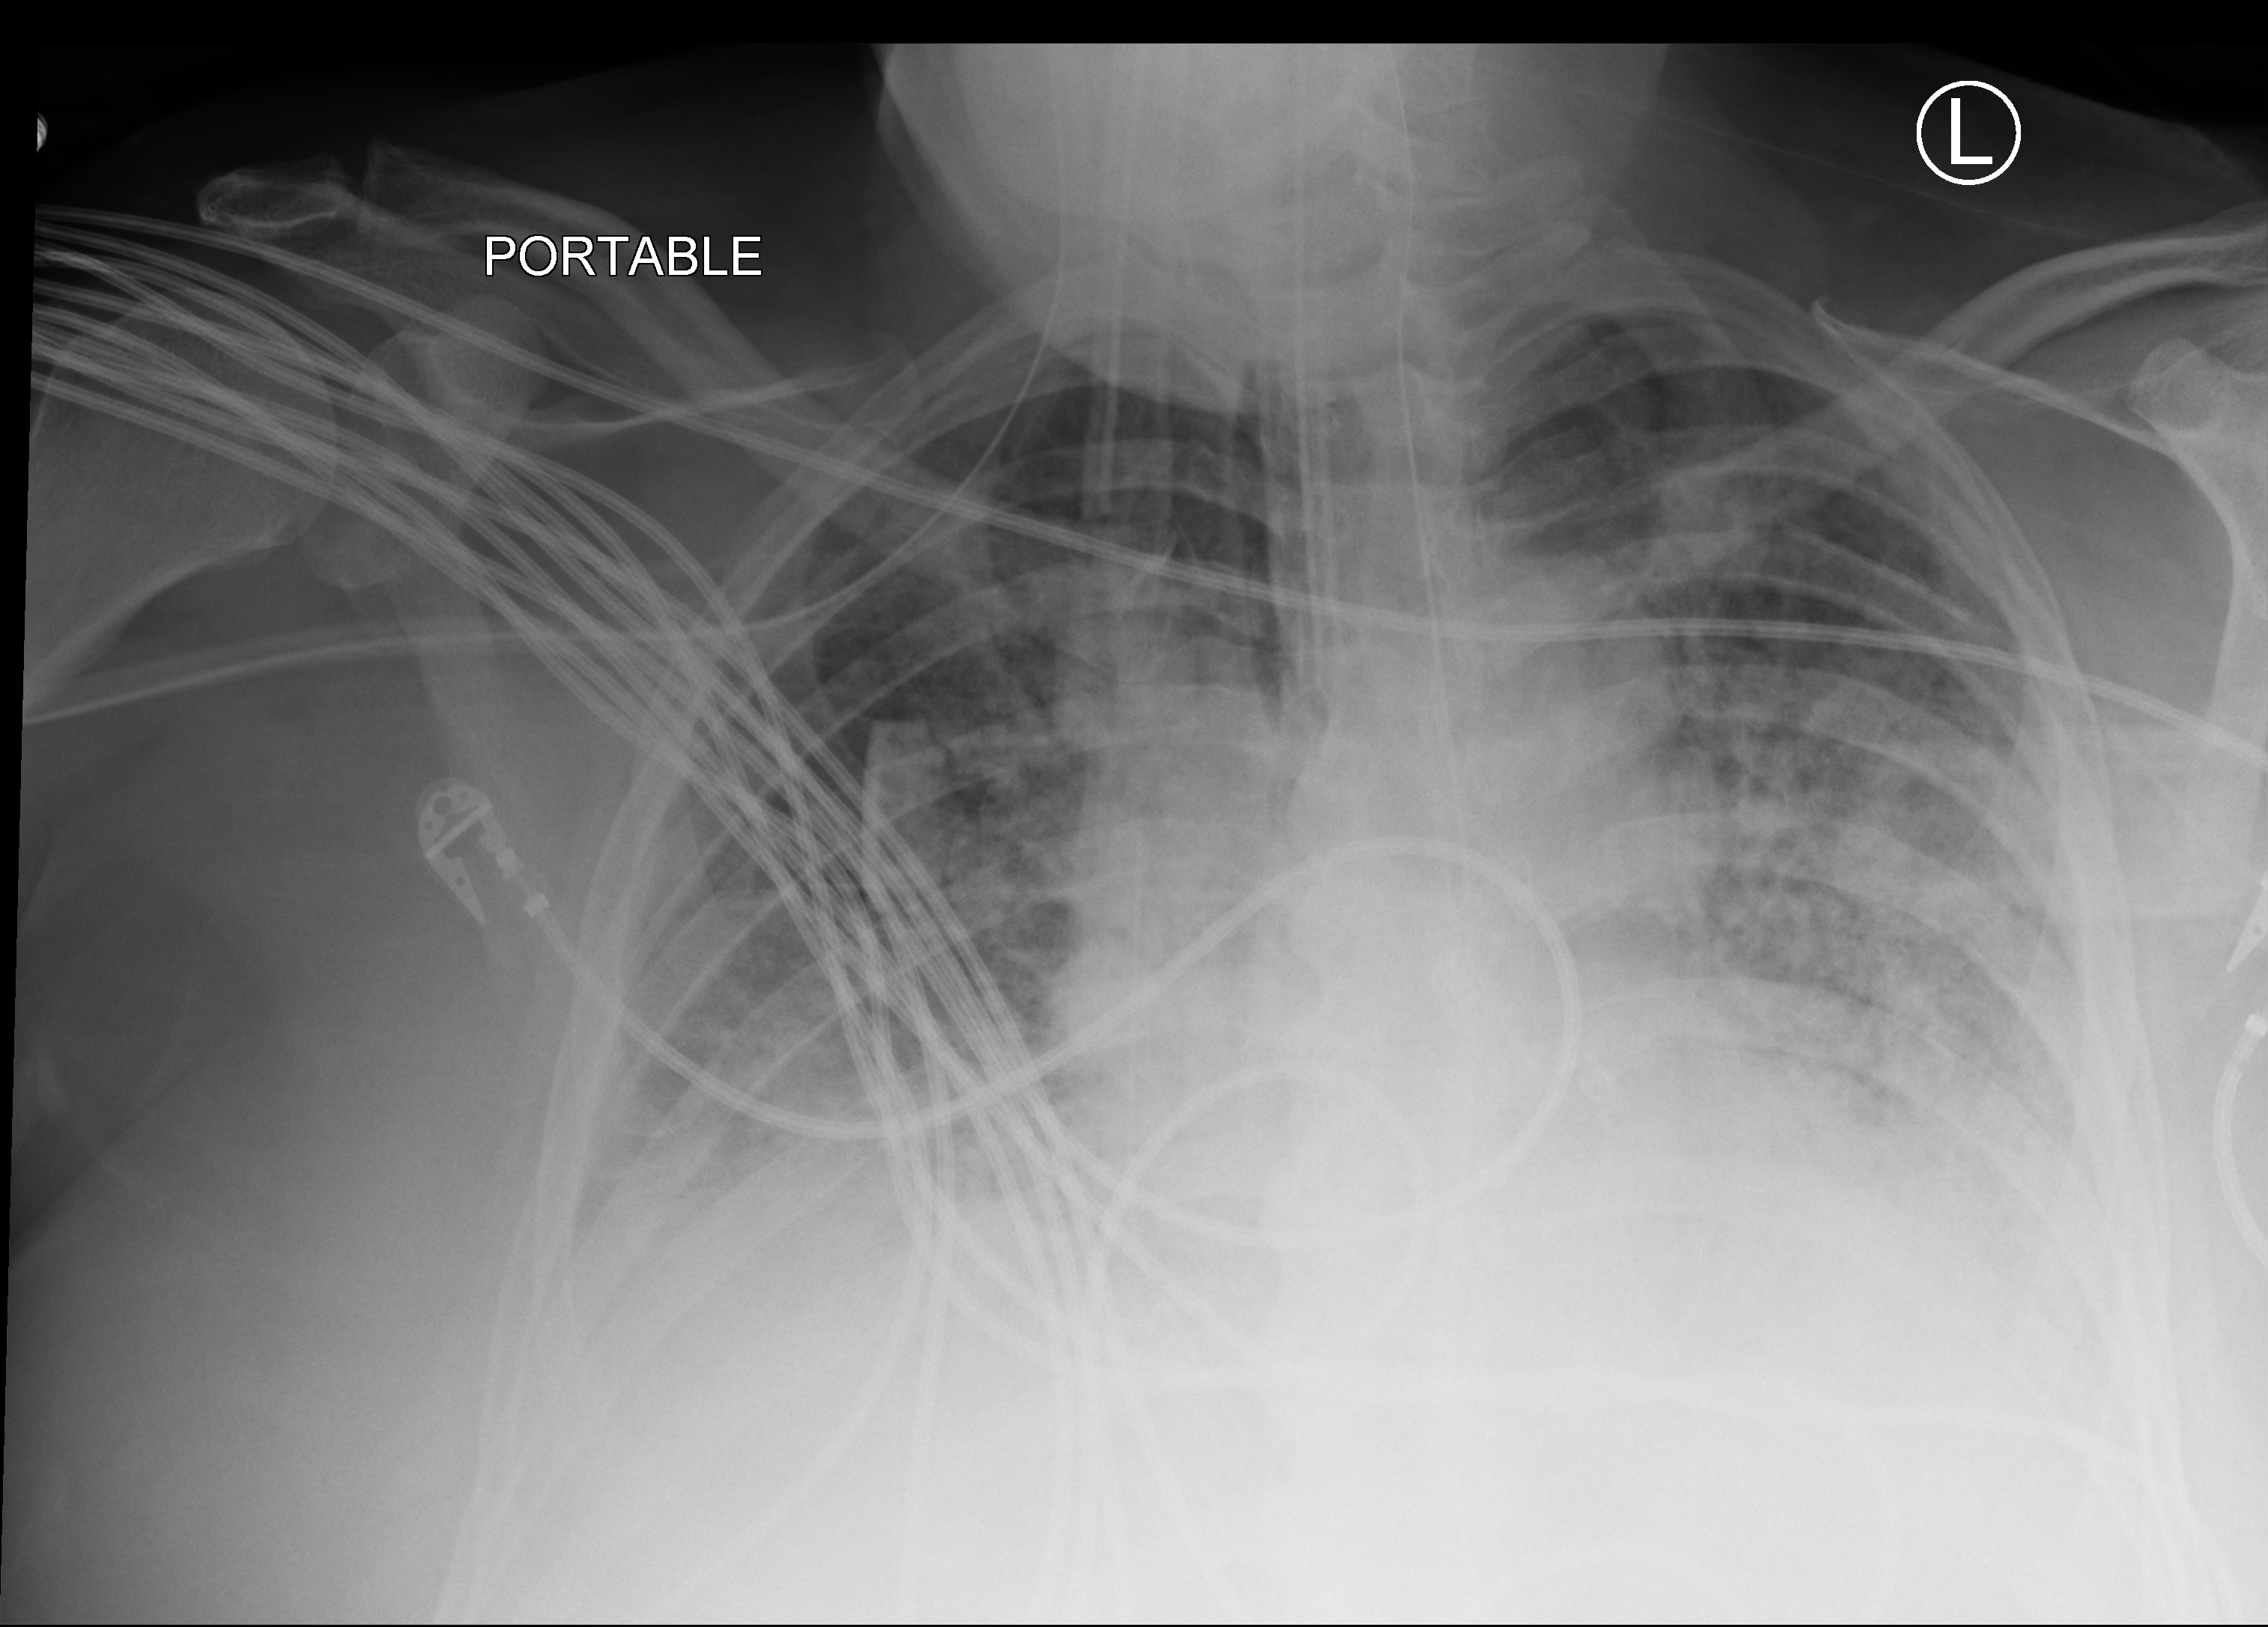
Bedside chest radiograph (computed radiography), anteroposterior (AP) projection. Patient hospitalised with COVID-19; male, aged 60–74 years.
From the hospital-stay record, not from the radiograph (when in the stay this image was taken is not recorded): mechanically ventilated during this hospital stay: yes; length of hospital stay: 40 days; admitted to intensive care during this hospital stay: yes.